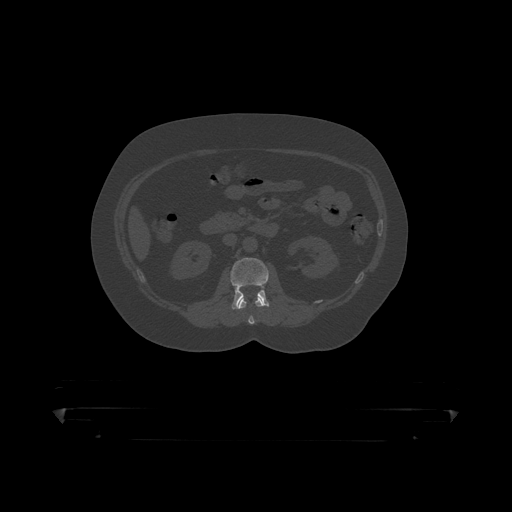
CT including the spine, one axial slice. Reconstruction kernel STANDARD. Bone window (W 1800 / L 400 HU). 1.25 mm slice thickness. 512 × 512 image matrix, field of view 650 × 650 mm. Male patient, age 60 years. Case-level facts recorded for this patient, not image findings: primary cancer: prostate.
Outlined on this slice (semi-automatically segmented with operator editing):
- L1 vertebra: box from (x=239, y=299) to (x=265, y=319) px
- L2 vertebra: (x=230, y=258)–(x=270, y=310)